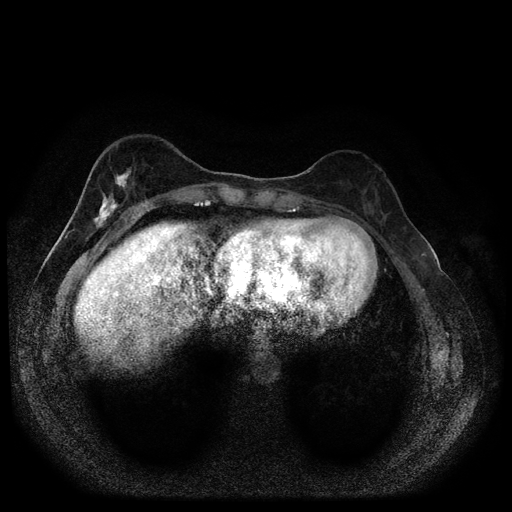
Breast MRI (dynamic contrast-enhanced, multi-phase), one axial slice. Position 32 of 116 along the scan axis. Dynamic contrast-enhanced series, time point 2 of 5 at this slice position (early post-contrast). 1.5 T. TE 2.7 ms, TR 5.4 ms. 2 mm slice thickness. 512 × 512 image matrix, field of view 330 × 330 mm. Female patient, age 49 years.
Outlined on this slice (semi-automatic segmentation, software-assisted and operator-edited):
- breast lesion (labelled 'tumour' in the annotation; benign lesions carry a separate 'benign' label): bounding box [x1, y1, x2, y2] px = [92, 164, 134, 231]